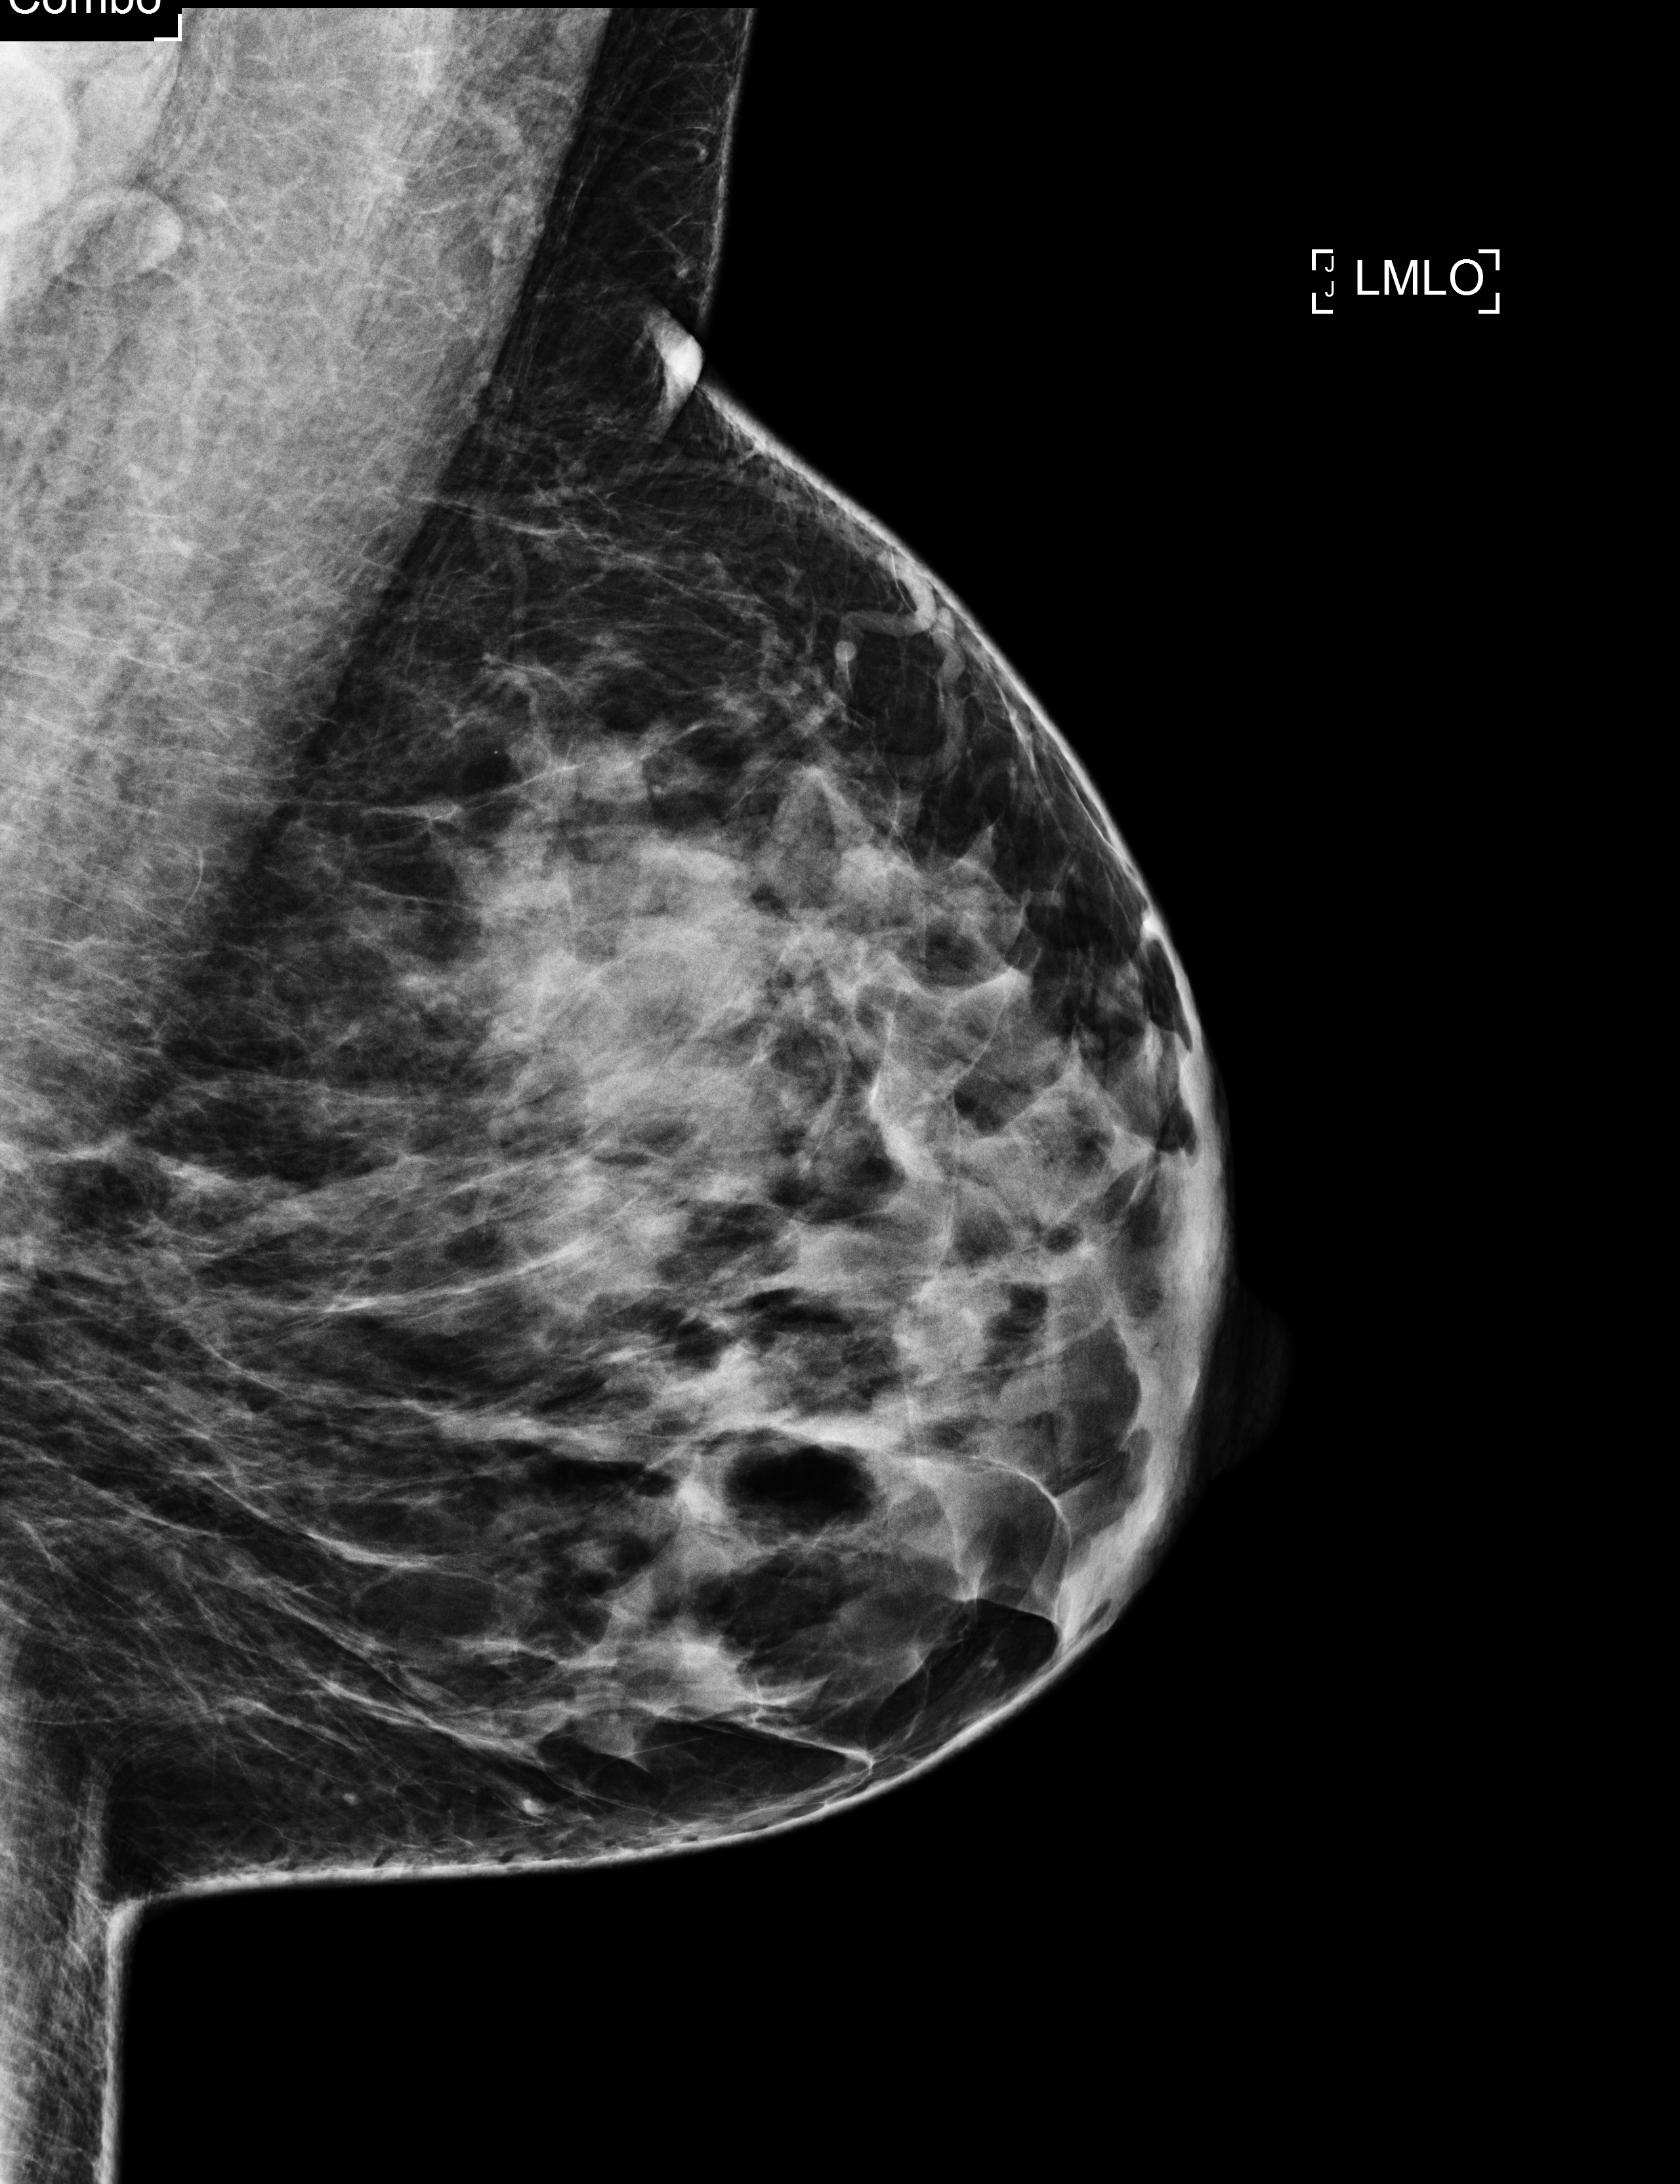
Full-field digital mammogram (FFDM), left breast, mediolateral oblique (MLO) view, screening examination, system: Selenia Dimensions. Patient aged 48 years (female).
BI-RADS breast density category at the screening exam (both breasts, scale 1–4): 3. Final BI-RADS category for the screening round (tomosynthesis exam, both breasts): category 1. Recall: no recall after this screen.